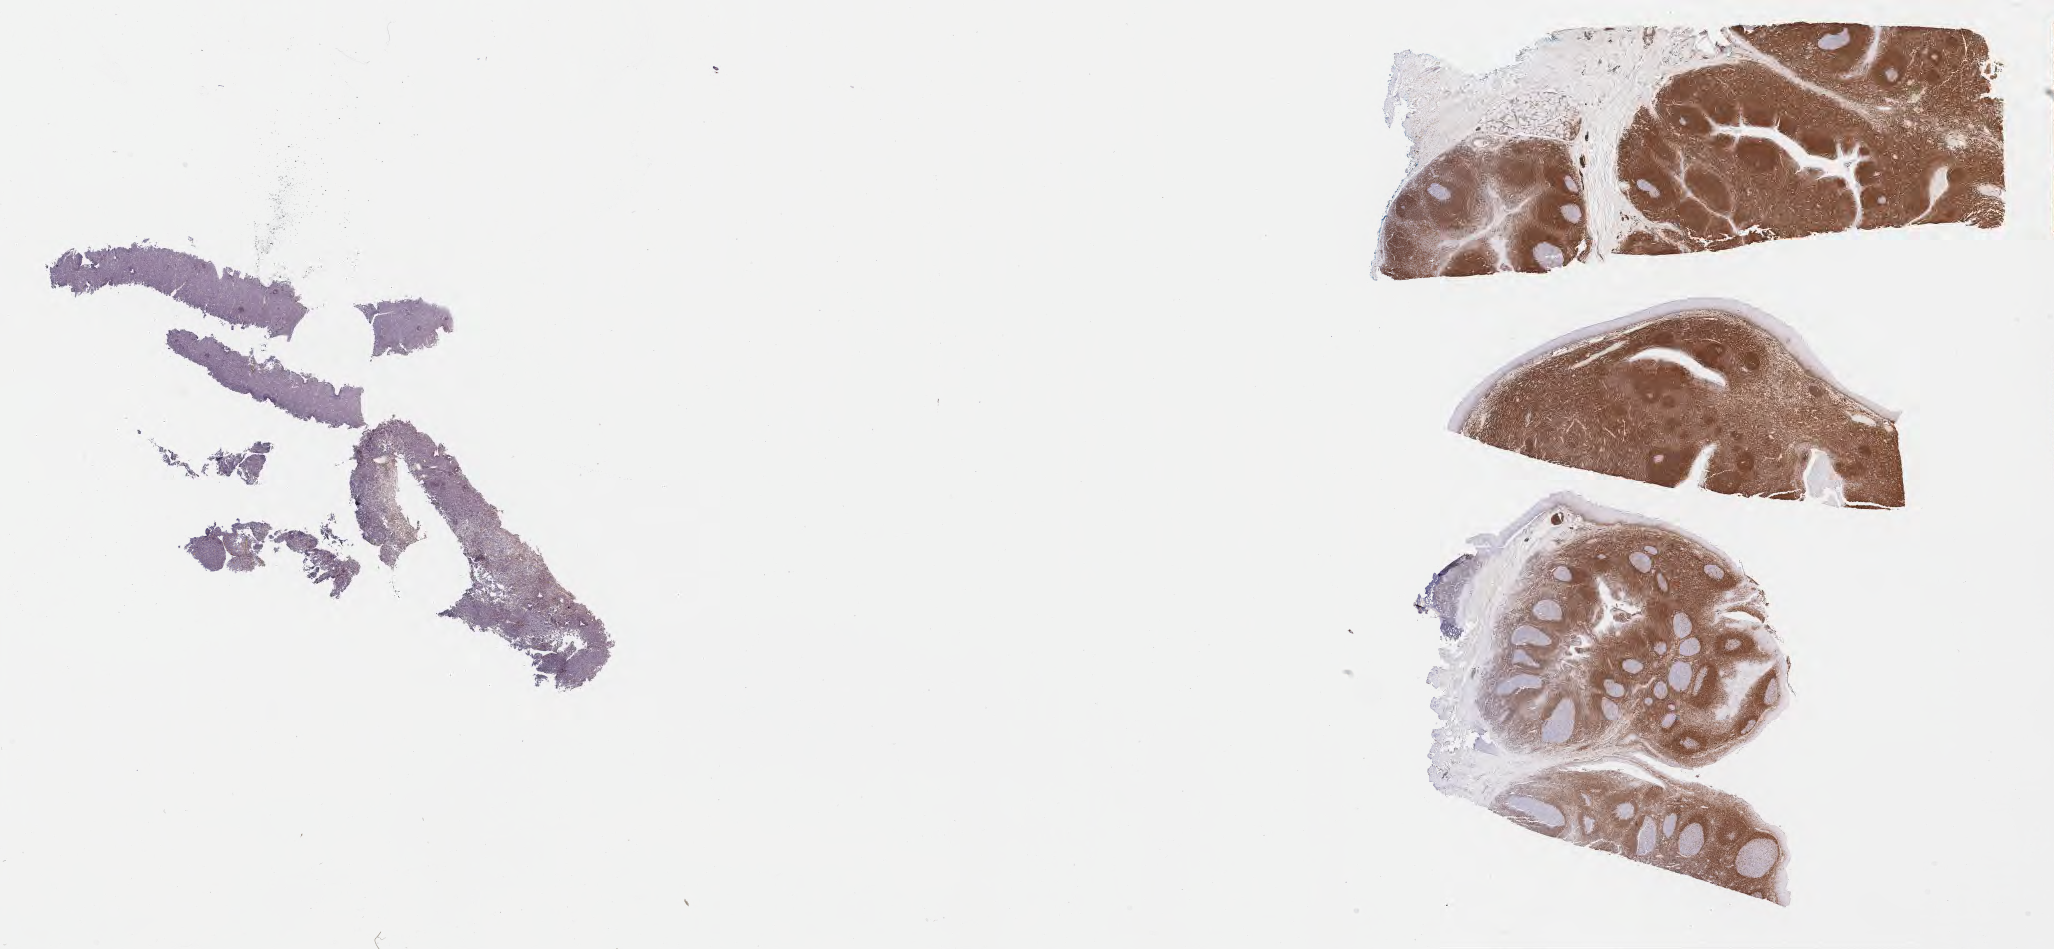
IHC for BCL2, whole-slide image, low-resolution overview of the scanned area, about 33.2 x 15.3 mm, specimen: tumor tissue, anatomic site: liver. Male, age 4 years at initial diagnosis.
Diagnosis: Burkitt lymphoma, NOS.